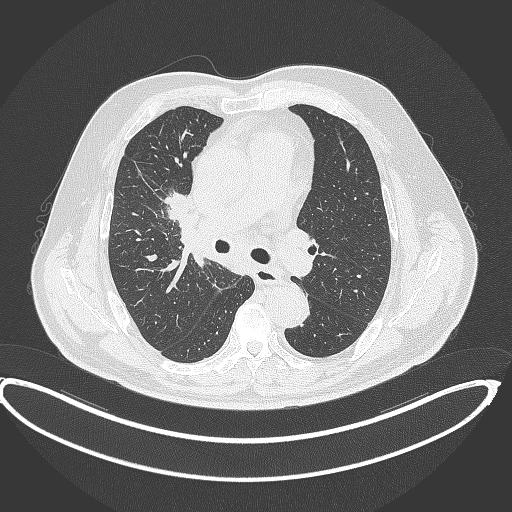
Chest CT, one axial slice. Slice 250 of 390 in the series (ordered by position). Lung window (W 1500 / L -600 HU). 512 × 512 image matrix, field of view 448 × 448 mm. Male patient, age 62 years. Case-level facts recorded for this patient, not image findings: clinical TNM (as recorded): T1c N3 M1c.
Outlined on this slice (bounding box drawn by a radiologist):
- lung tumour (recorded histology: adenocarcinoma): bounding box <162,190,194,221> (left, top, right, bottom; pixels)